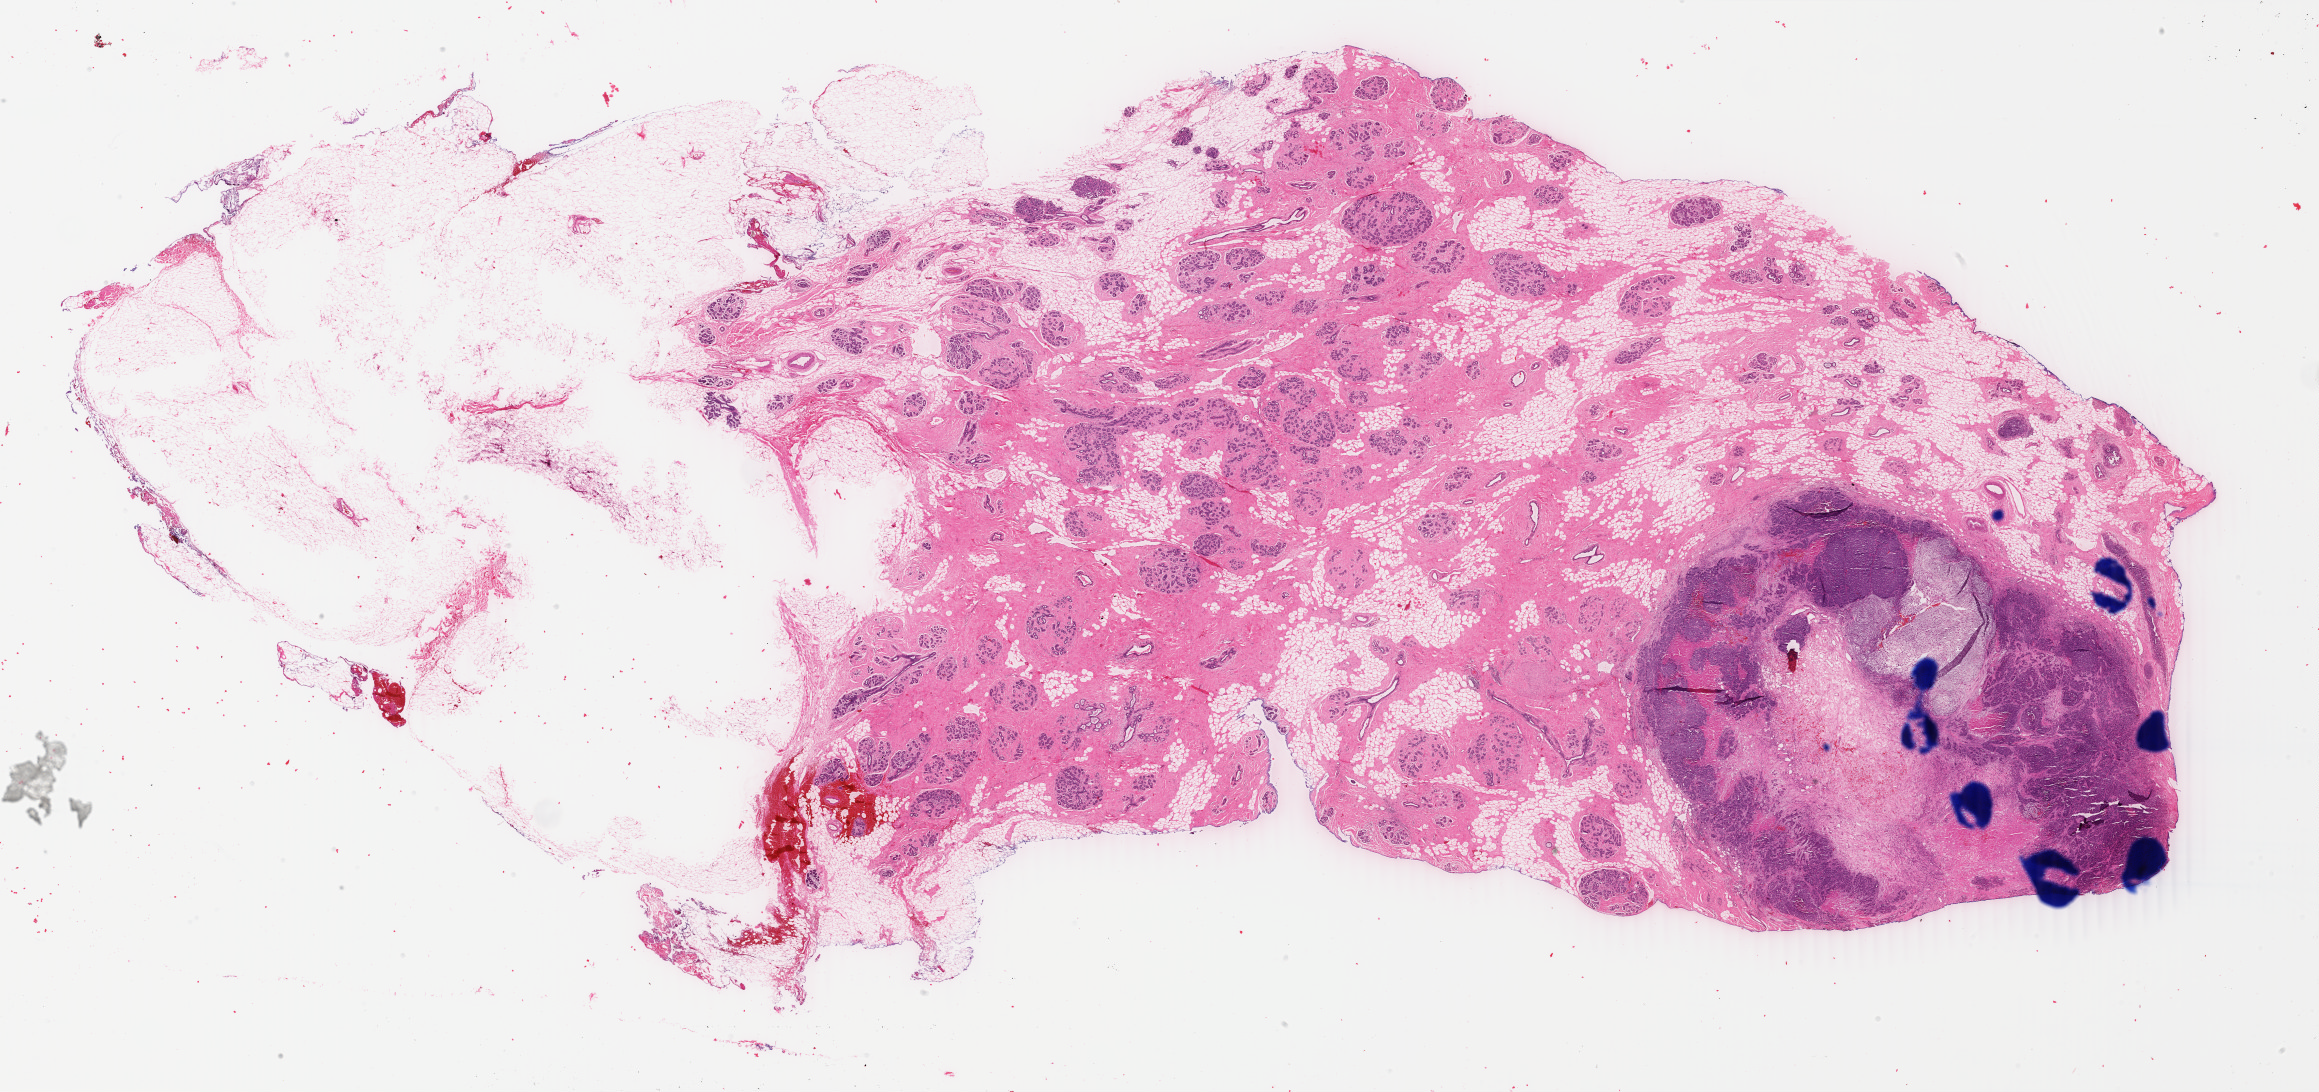
Digitized H&E-stained tissue section (whole slide), low-resolution overview of the scanned area, about 36.9 x 17.4 mm; FFPE section; primary tumour sample from the breast. Female, age 40 years at initial diagnosis.
Lymph nodes positive (case pathology): 0 of 15 examined. AJCC pathologic stage: IA (3rd edition). Pathologic diagnosis: Infiltrating duct mixed with other types of carcinoma.